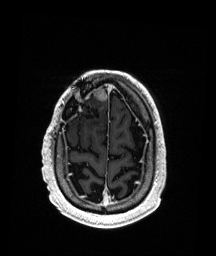
Brain MRI from a brain-tumour surgery series, one axial slice; slice 40 of 192 in the series (ordered by position); T1-weighted post-contrast; 1 mm slice thickness; 216 × 256 image matrix, field of view 211 × 250 mm. From the clinical record (not read from this slice): histopathology: Astrocytoma; WHO grade: 3; IDH mutation: yes; tumour location: Right Frontal.
Outlined on this slice (outlined manually by an expert reader):
- previous resection cavity: bounding box <76,106,101,120> (left, top, right, bottom; pixels)
- tumour: <93,87,108,101>